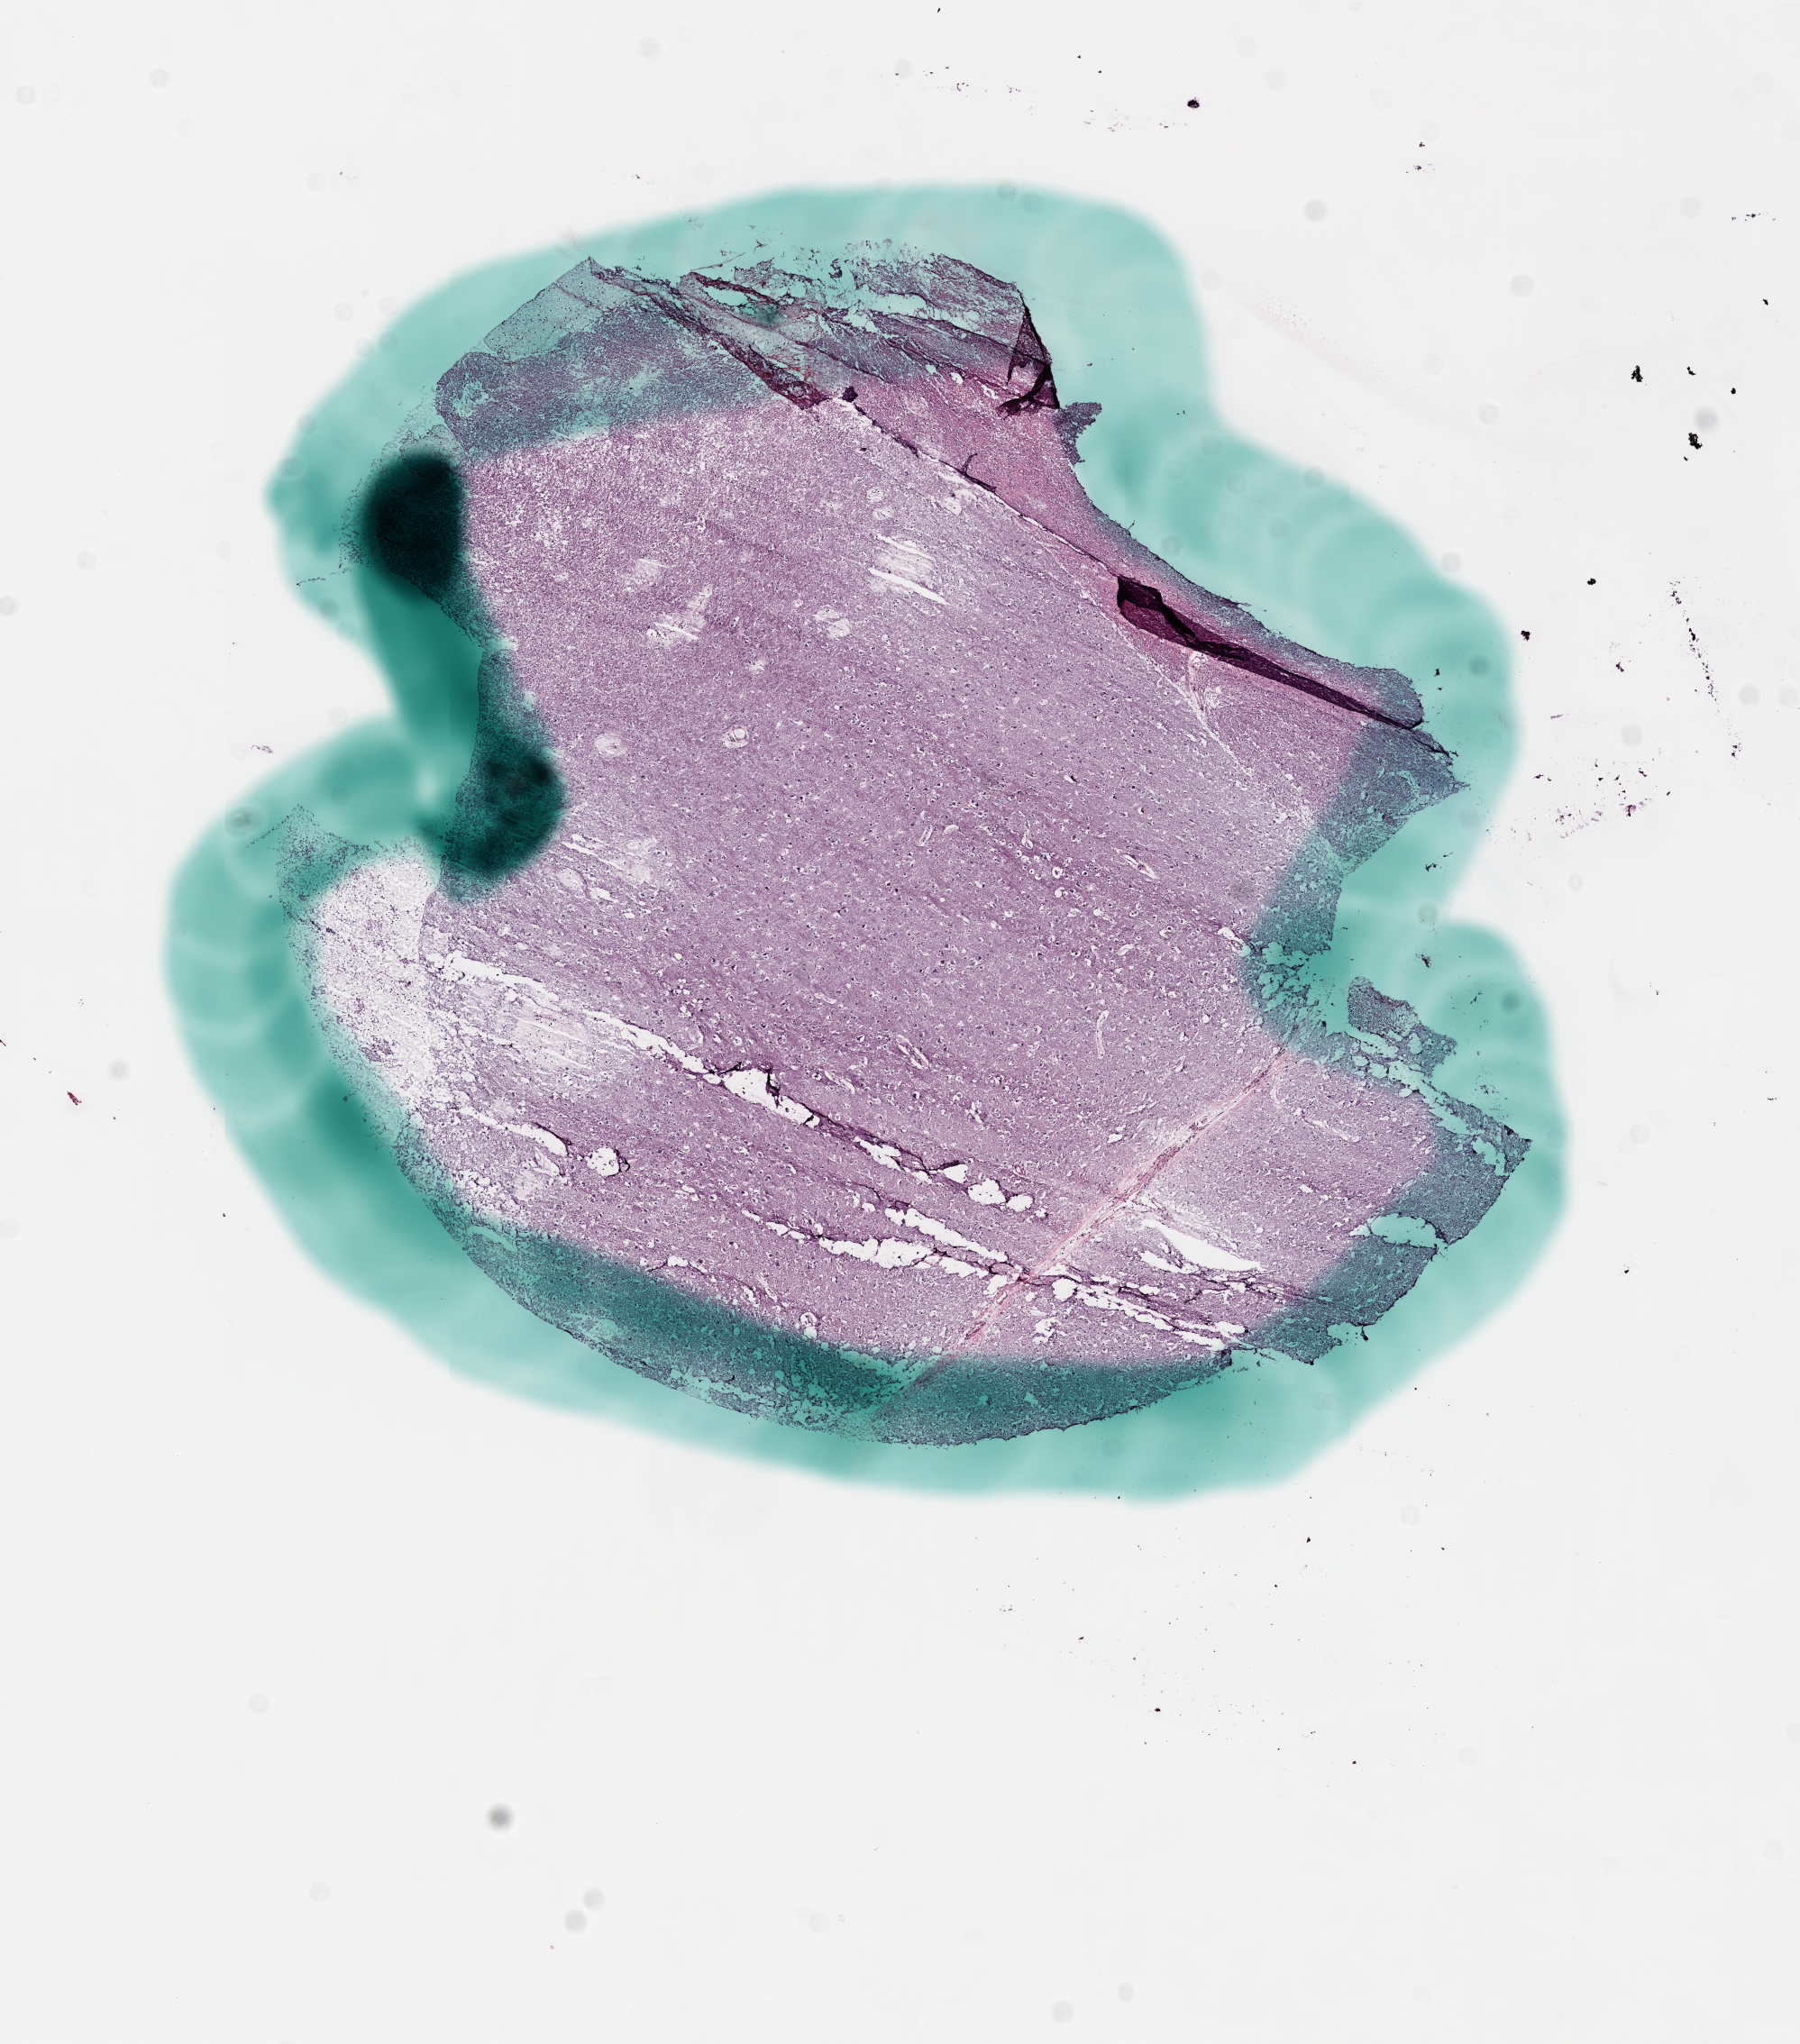
Digitized H&E-stained tissue section (whole slide), low-resolution overview of the scanned area, about 8.0 x 9.1 mm; frozen section from the bottom of the tissue portion; primary tumour sample from the brain. Male patient; age at initial diagnosis 52 years. Composition of this section per pathologist review: tumour cells 0%, tumour nuclei 0%, normal cells 100%, stromal cells 0%, necrosis 0%.
Histologic diagnosis: Glioblastoma.